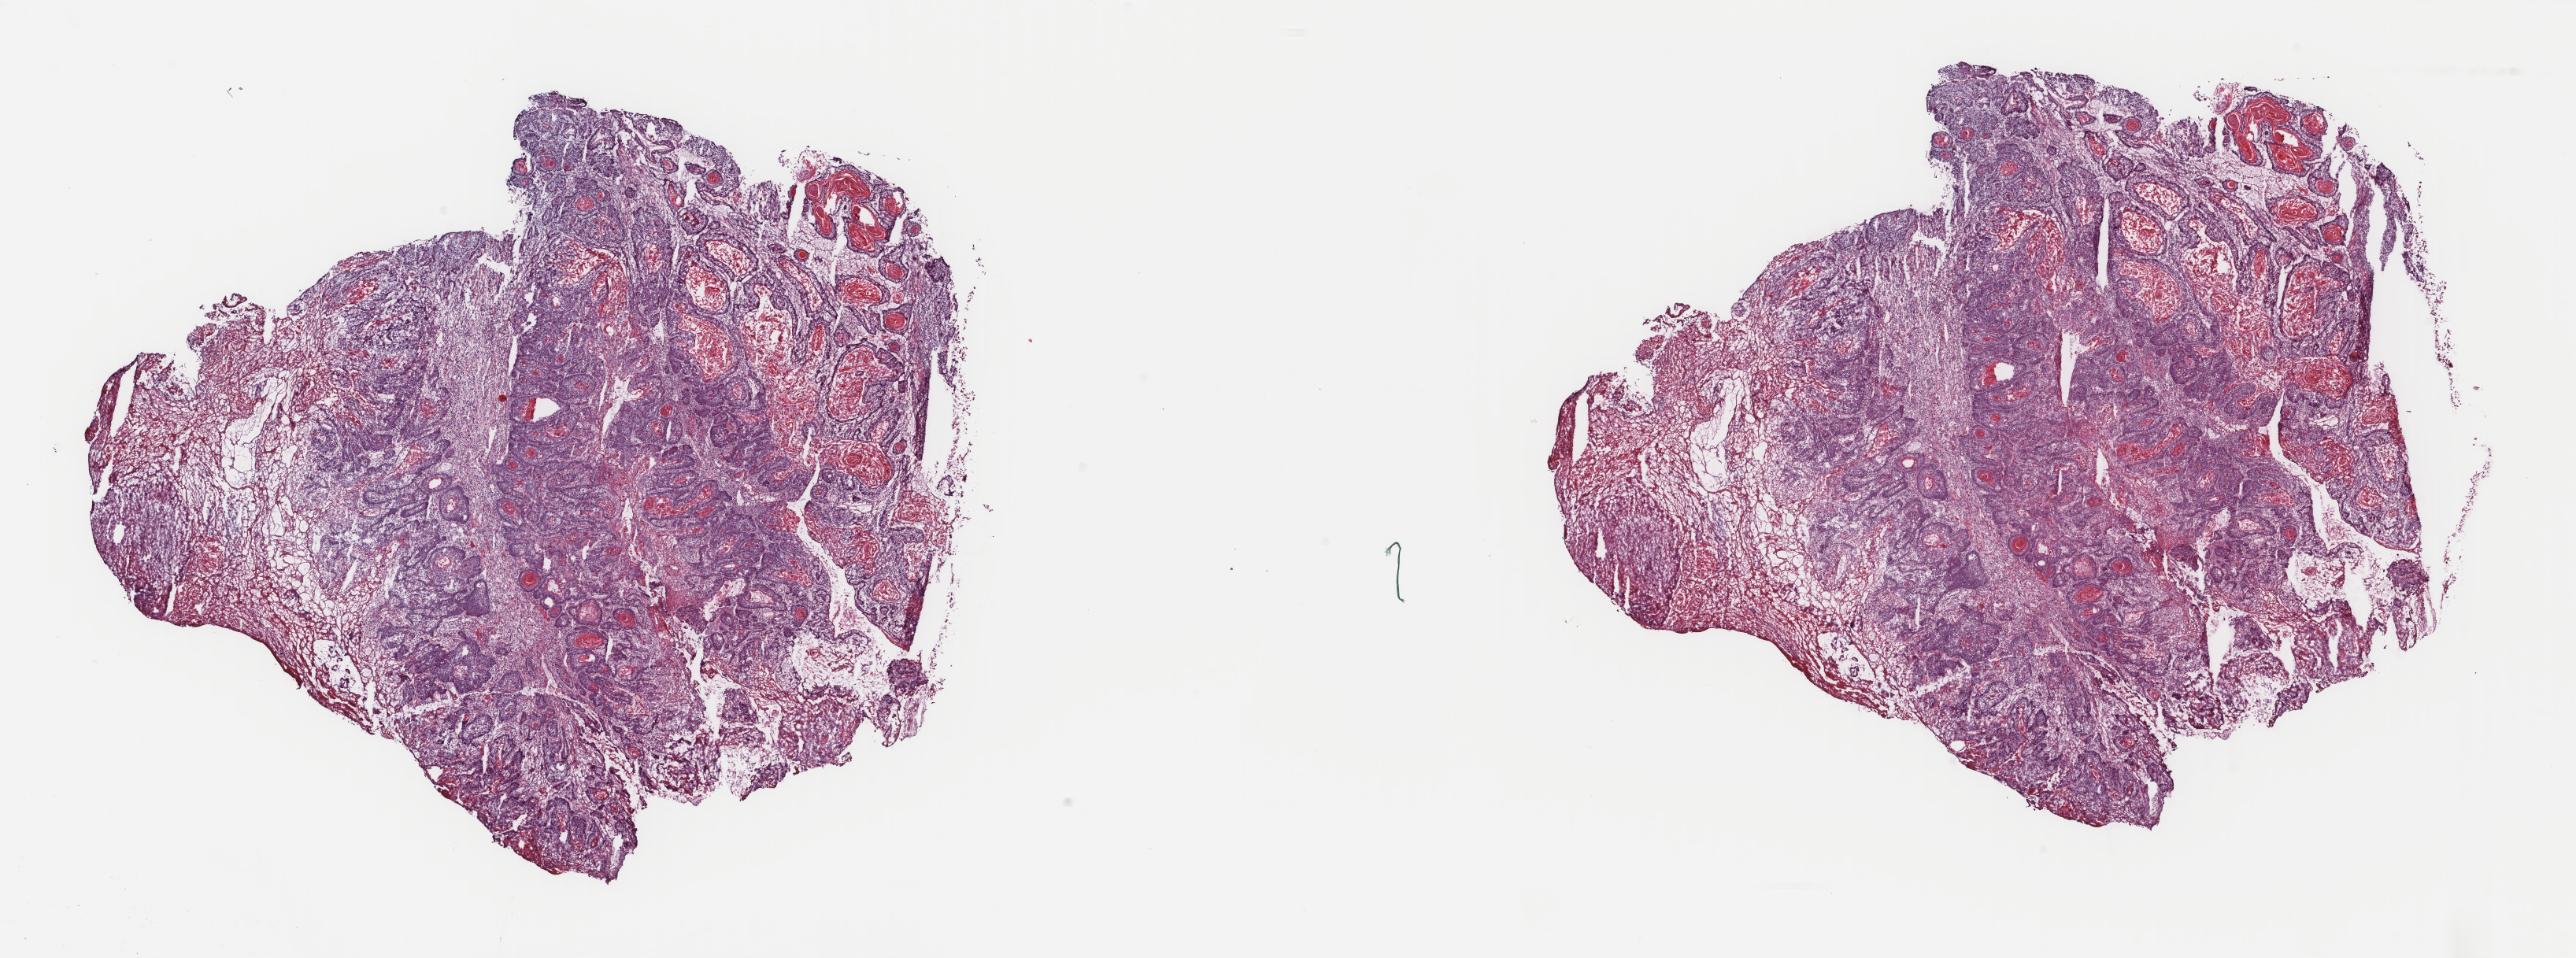
Whole-slide histology image, H&E, low-resolution overview of the scanned area, about 26.0 x 9.7 mm (acquisition: 40x scan). Frozen section from the top of the tissue portion. Head and neck, primary tumour sample. Female patient; age at initial diagnosis 70 years. Histologic grade: G2 (moderately differentiated). Slide review estimates, as recorded: tumour cells 80%, tumour nuclei 75%, normal cells 0%, stromal cells 10%, necrosis 10%. Infiltration values recorded for this section: lymphocyte infiltration 5%, monocyte infiltration 0%, neutrophil infiltration 0%.
AJCC pathologic stage: II. Histologic diagnosis: Squamous cell carcinoma, keratinizing, NOS (tongue, NOS).